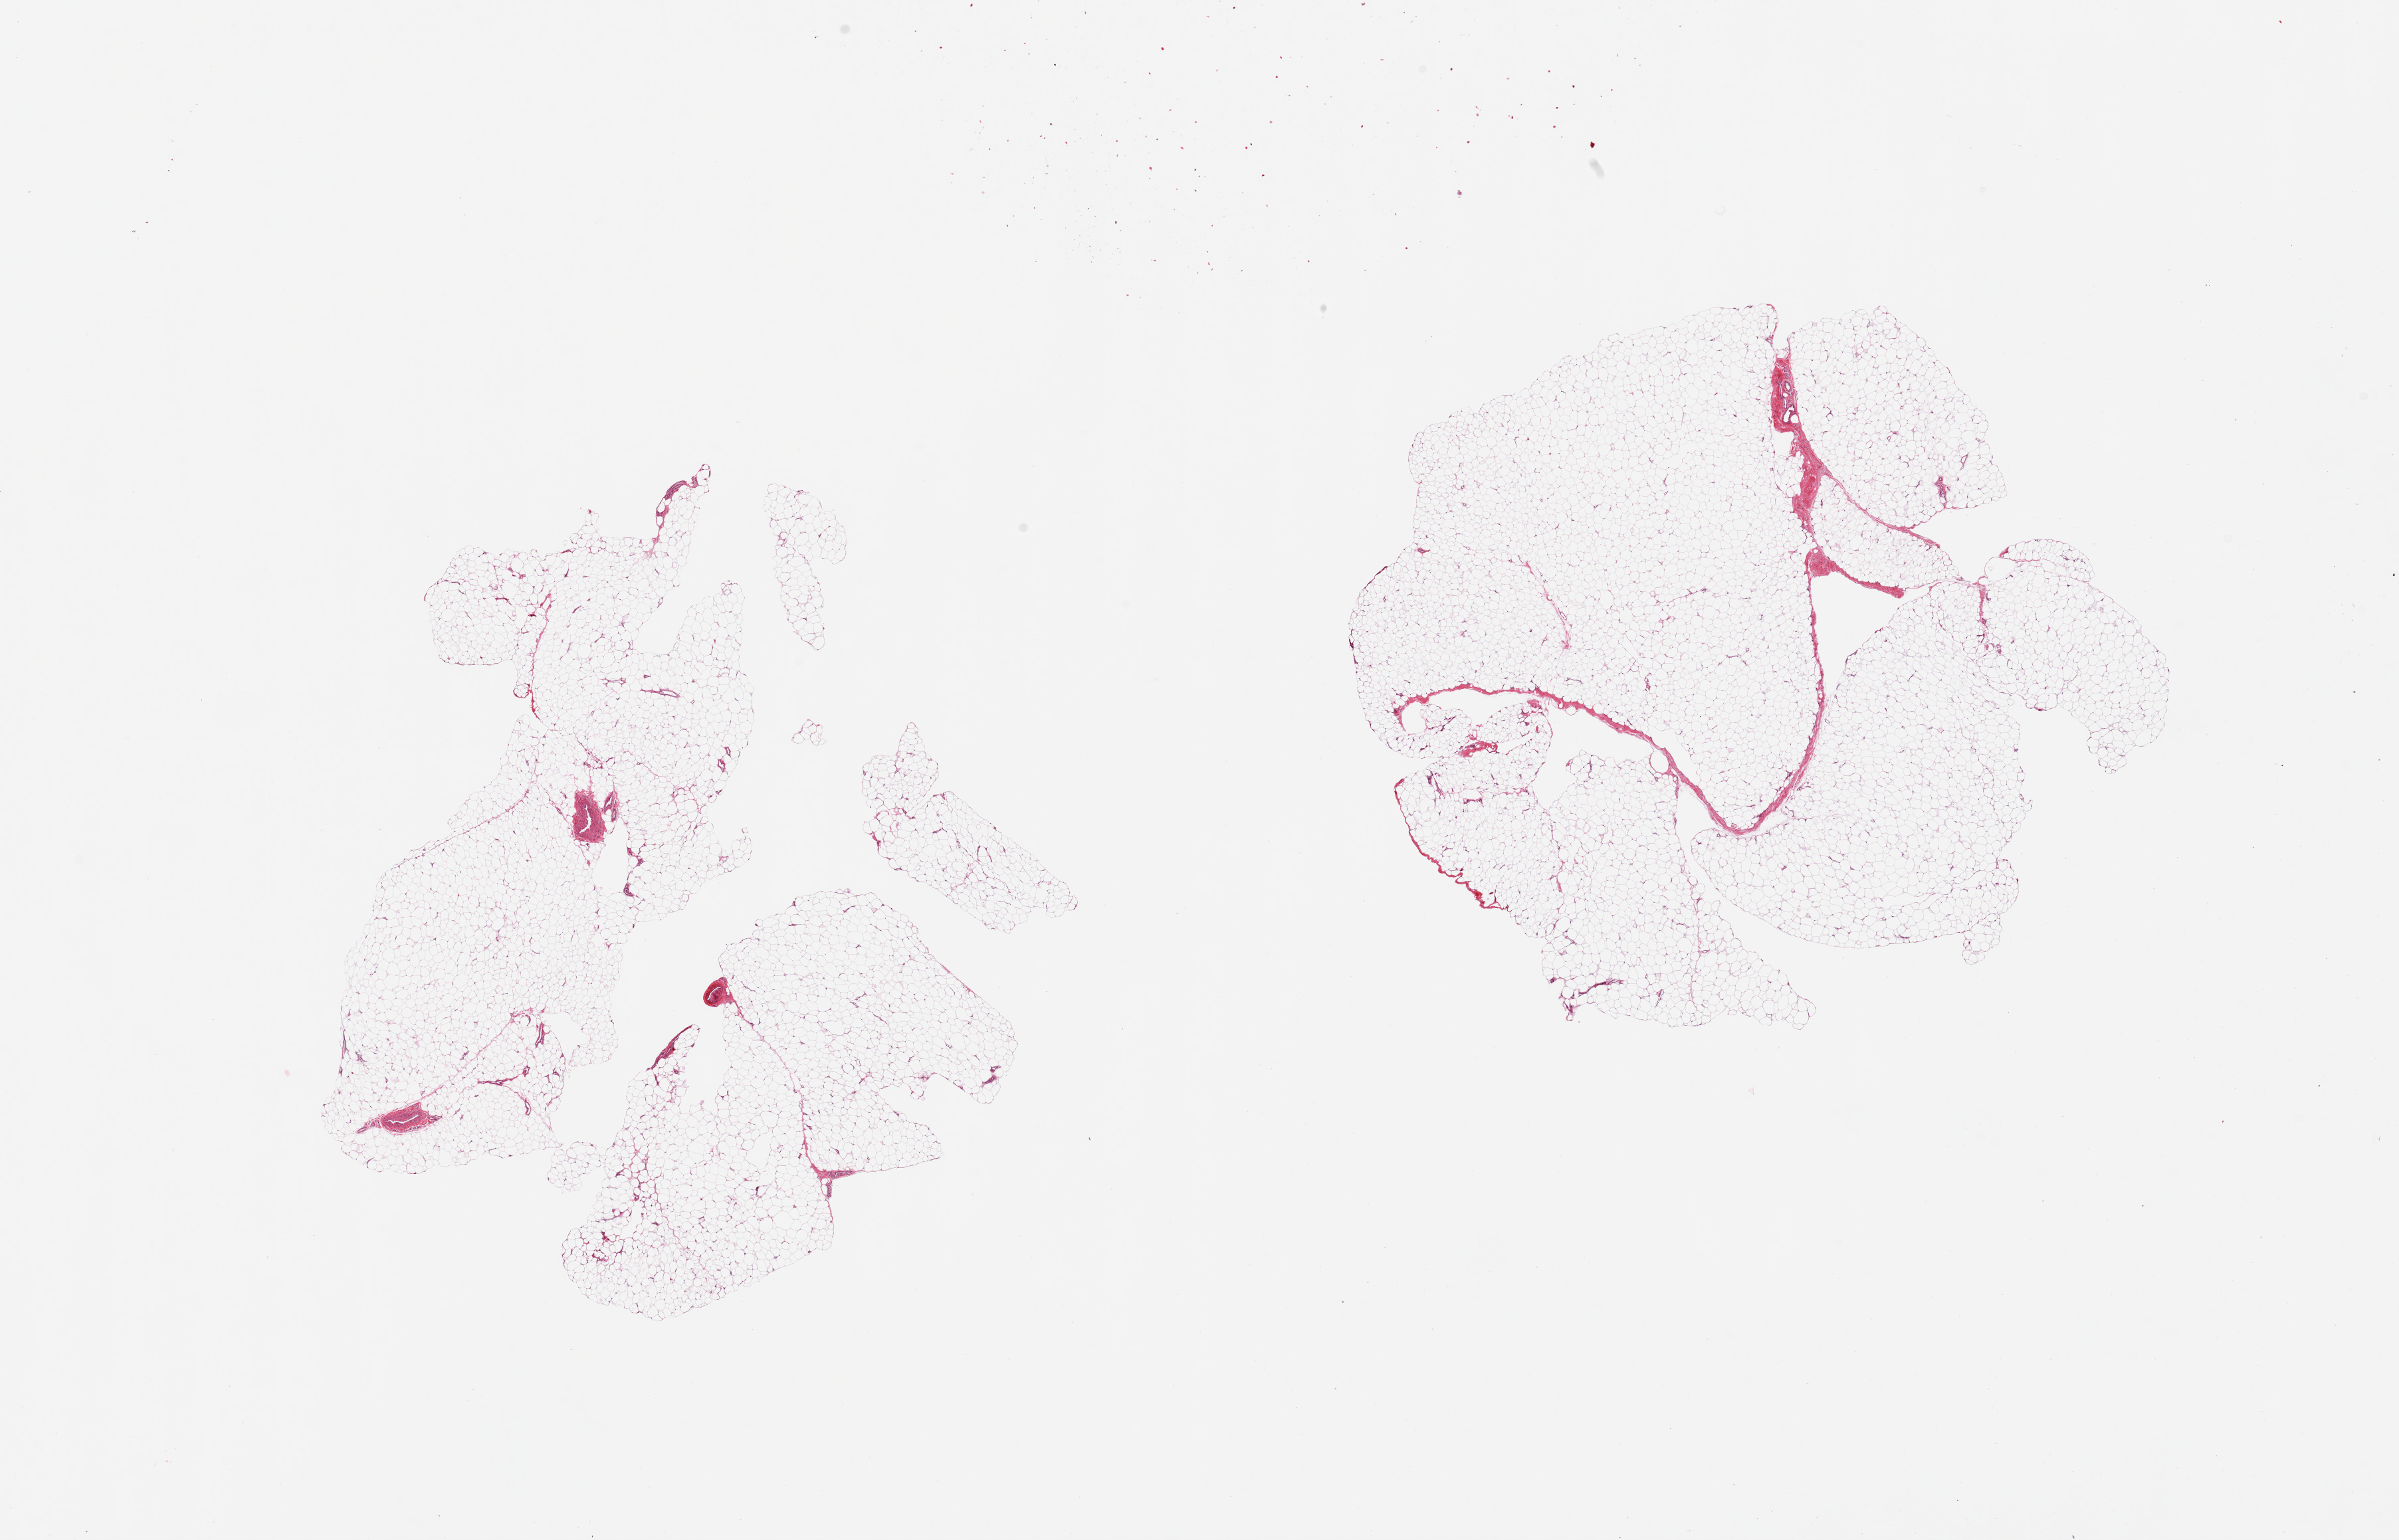
Whole-slide image, haematoxylin and eosin stain, whole scanned area (about 28.5 x 18.3 mm) shown as a low-resolution overview, PAXgene-fixed paraffin-embedded (PFPE) section, sampled site (target tissue): adipose tissue, donor tissue sample.
Review note (as recorded): 2 pieces.